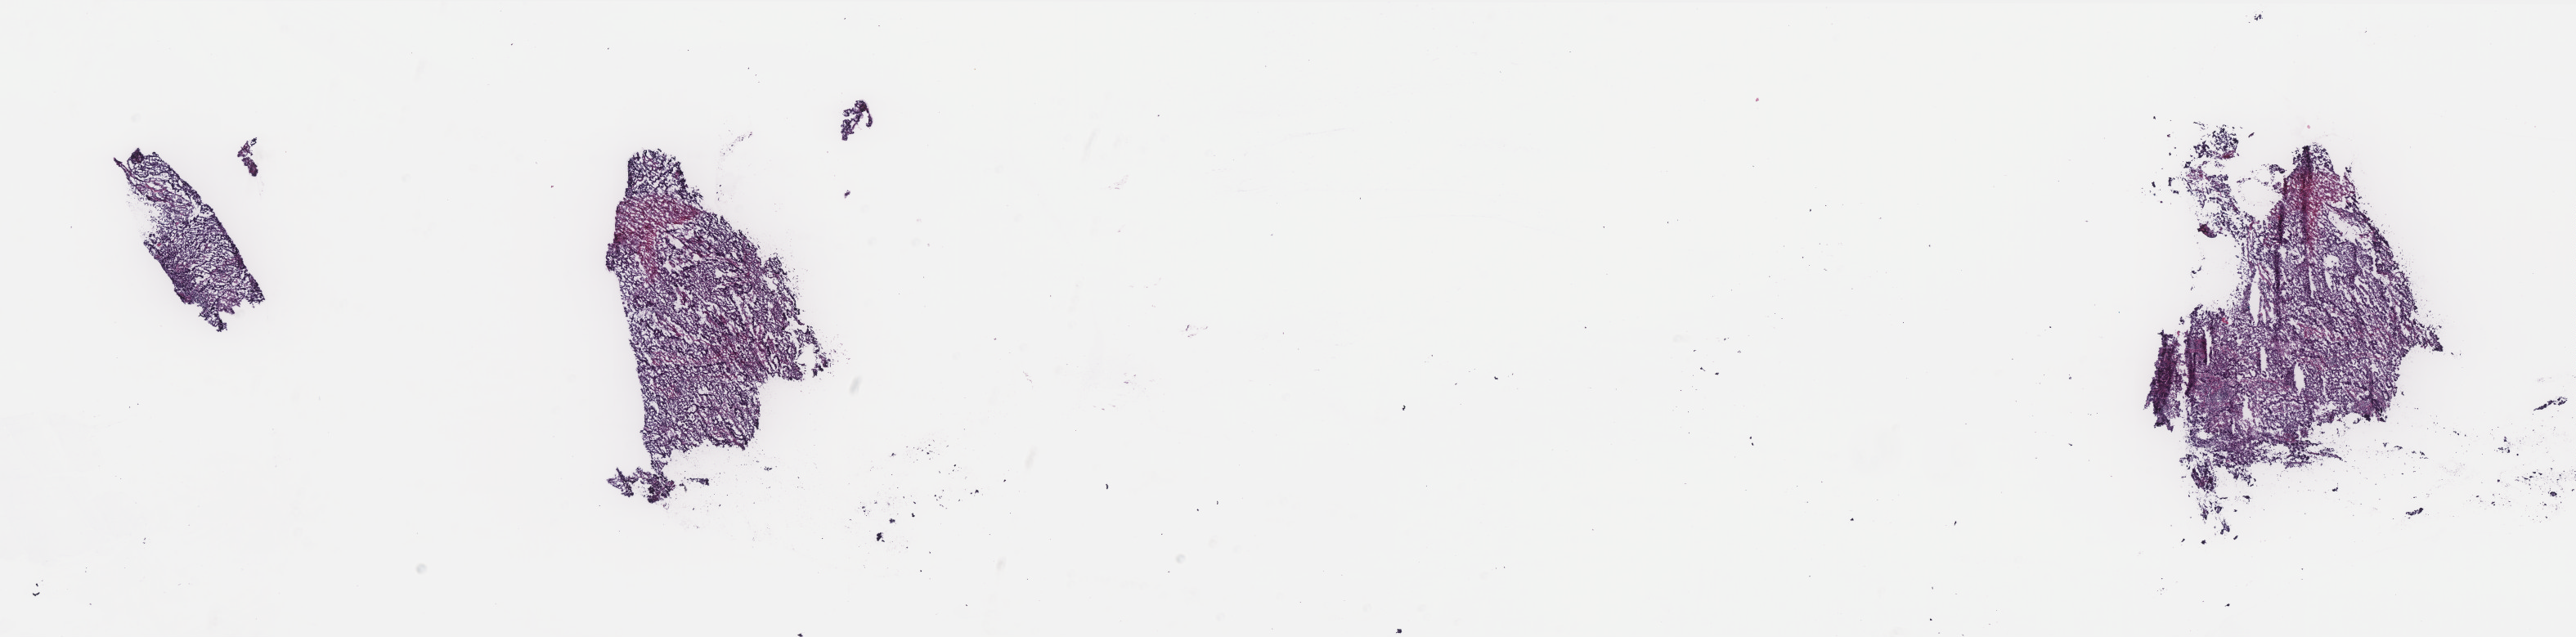
H&E-stained whole-slide image — low-resolution overview of the scanned area, about 25.3 x 6.2 mm; frozen section; sample: primary tumour, uterus. Female, age 62 years at initial diagnosis. Histologic grade: G3 (poorly differentiated). Slide review estimates, as recorded: tumour cells 85%, tumour nuclei 80%, normal cells 0%, stromal cells 0%, necrosis 15%. Inflammatory infiltration, as recorded: lymphocyte infiltration 0%, monocyte infiltration 0%, neutrophil infiltration 0%.
FIGO stage: IA. Pathologic diagnosis: Endometrioid adenocarcinoma, NOS (endometrium).